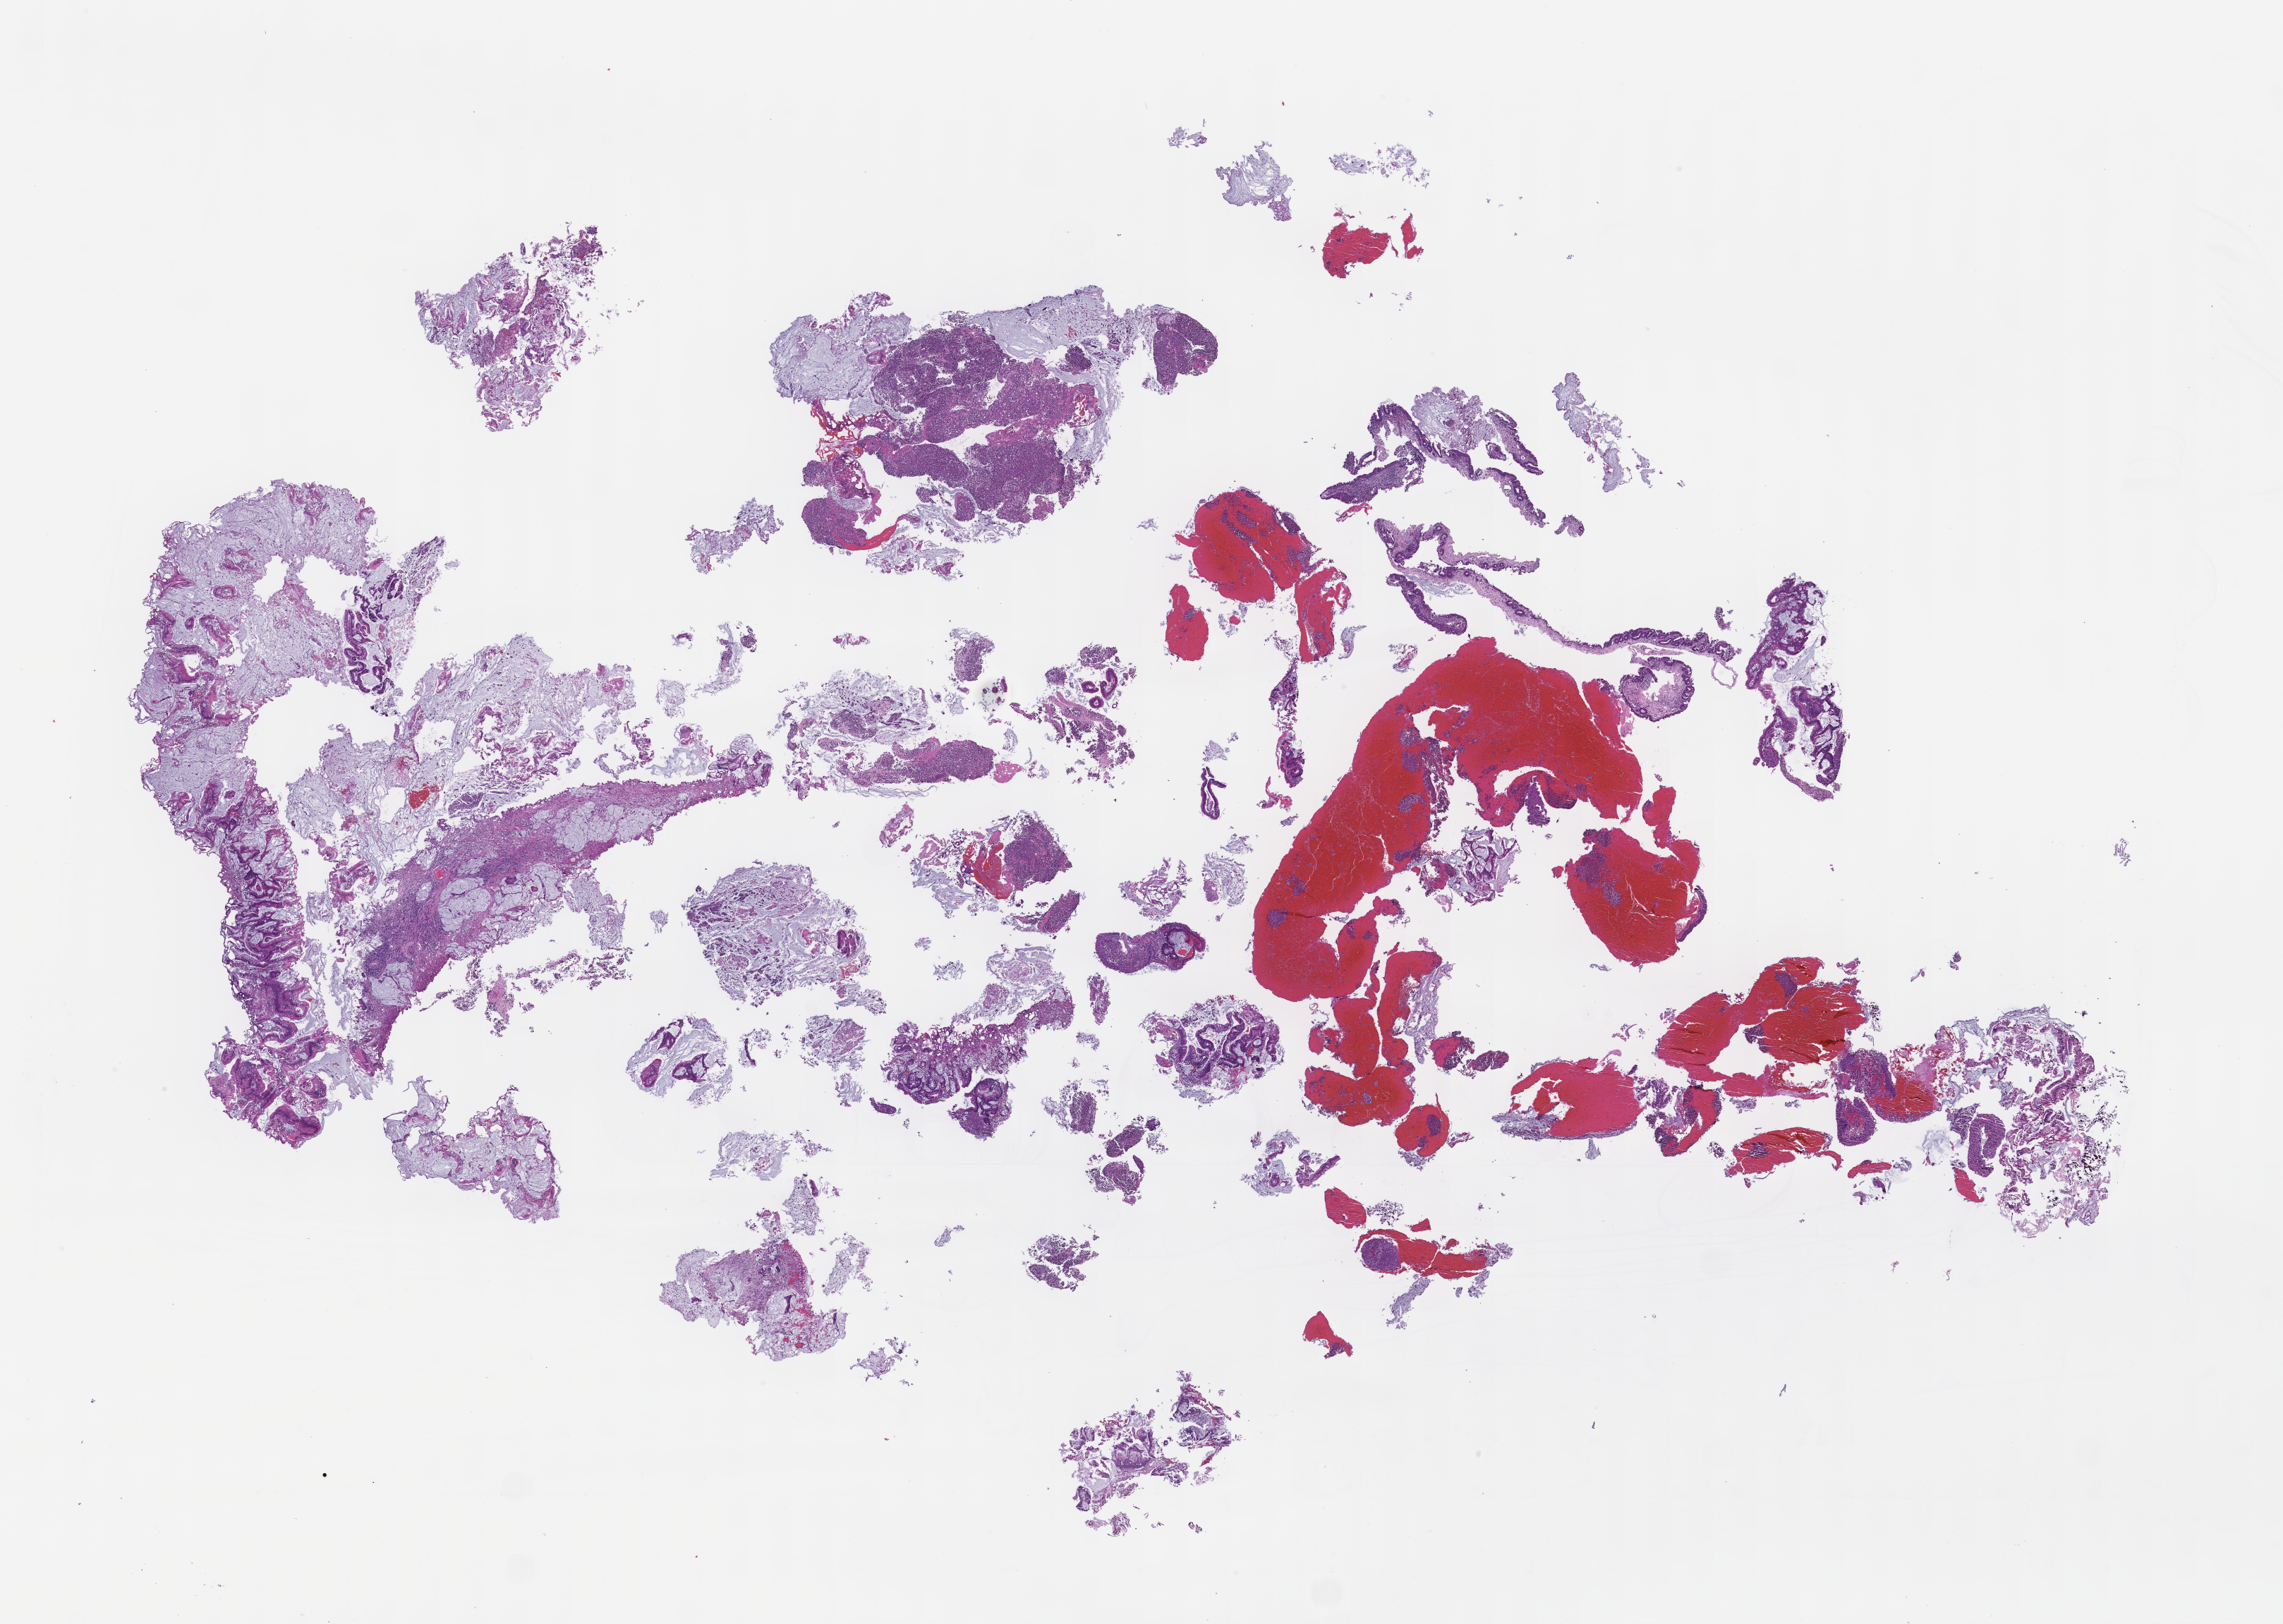
Digitized hematoxylin and eosin (H&E)-stained section, whole scanned area (about 26.1 x 18.6 mm) shown as a low-resolution overview, FFPE section, archival tissue. Male patient.
This section: metastasis (sampled organ not recorded). Primary diagnosis of the patient: Colorectal Carcinoma.